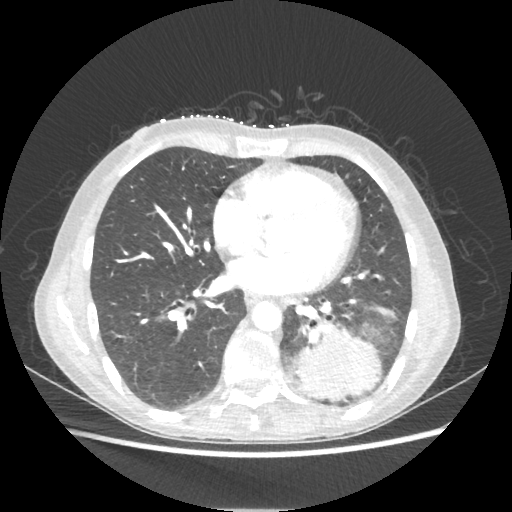
Chest CT, one axial slice. Slice 93 of 221 in the series (ordered by position). Reconstruction kernel STANDARD. 80 kVp. Lung window (W 1500 / L -600 HU). 512 × 512 image matrix. Female patient, age 53 years. Case-level facts recorded for this patient, not image findings: clinical TNM (as recorded): T3 N0 M0.
Annotated regions visible in this slice (bounding box drawn by a radiologist):
- lung tumour (recorded histology: adenocarcinoma): bounding box <292,319,380,401> (left, top, right, bottom; pixels)